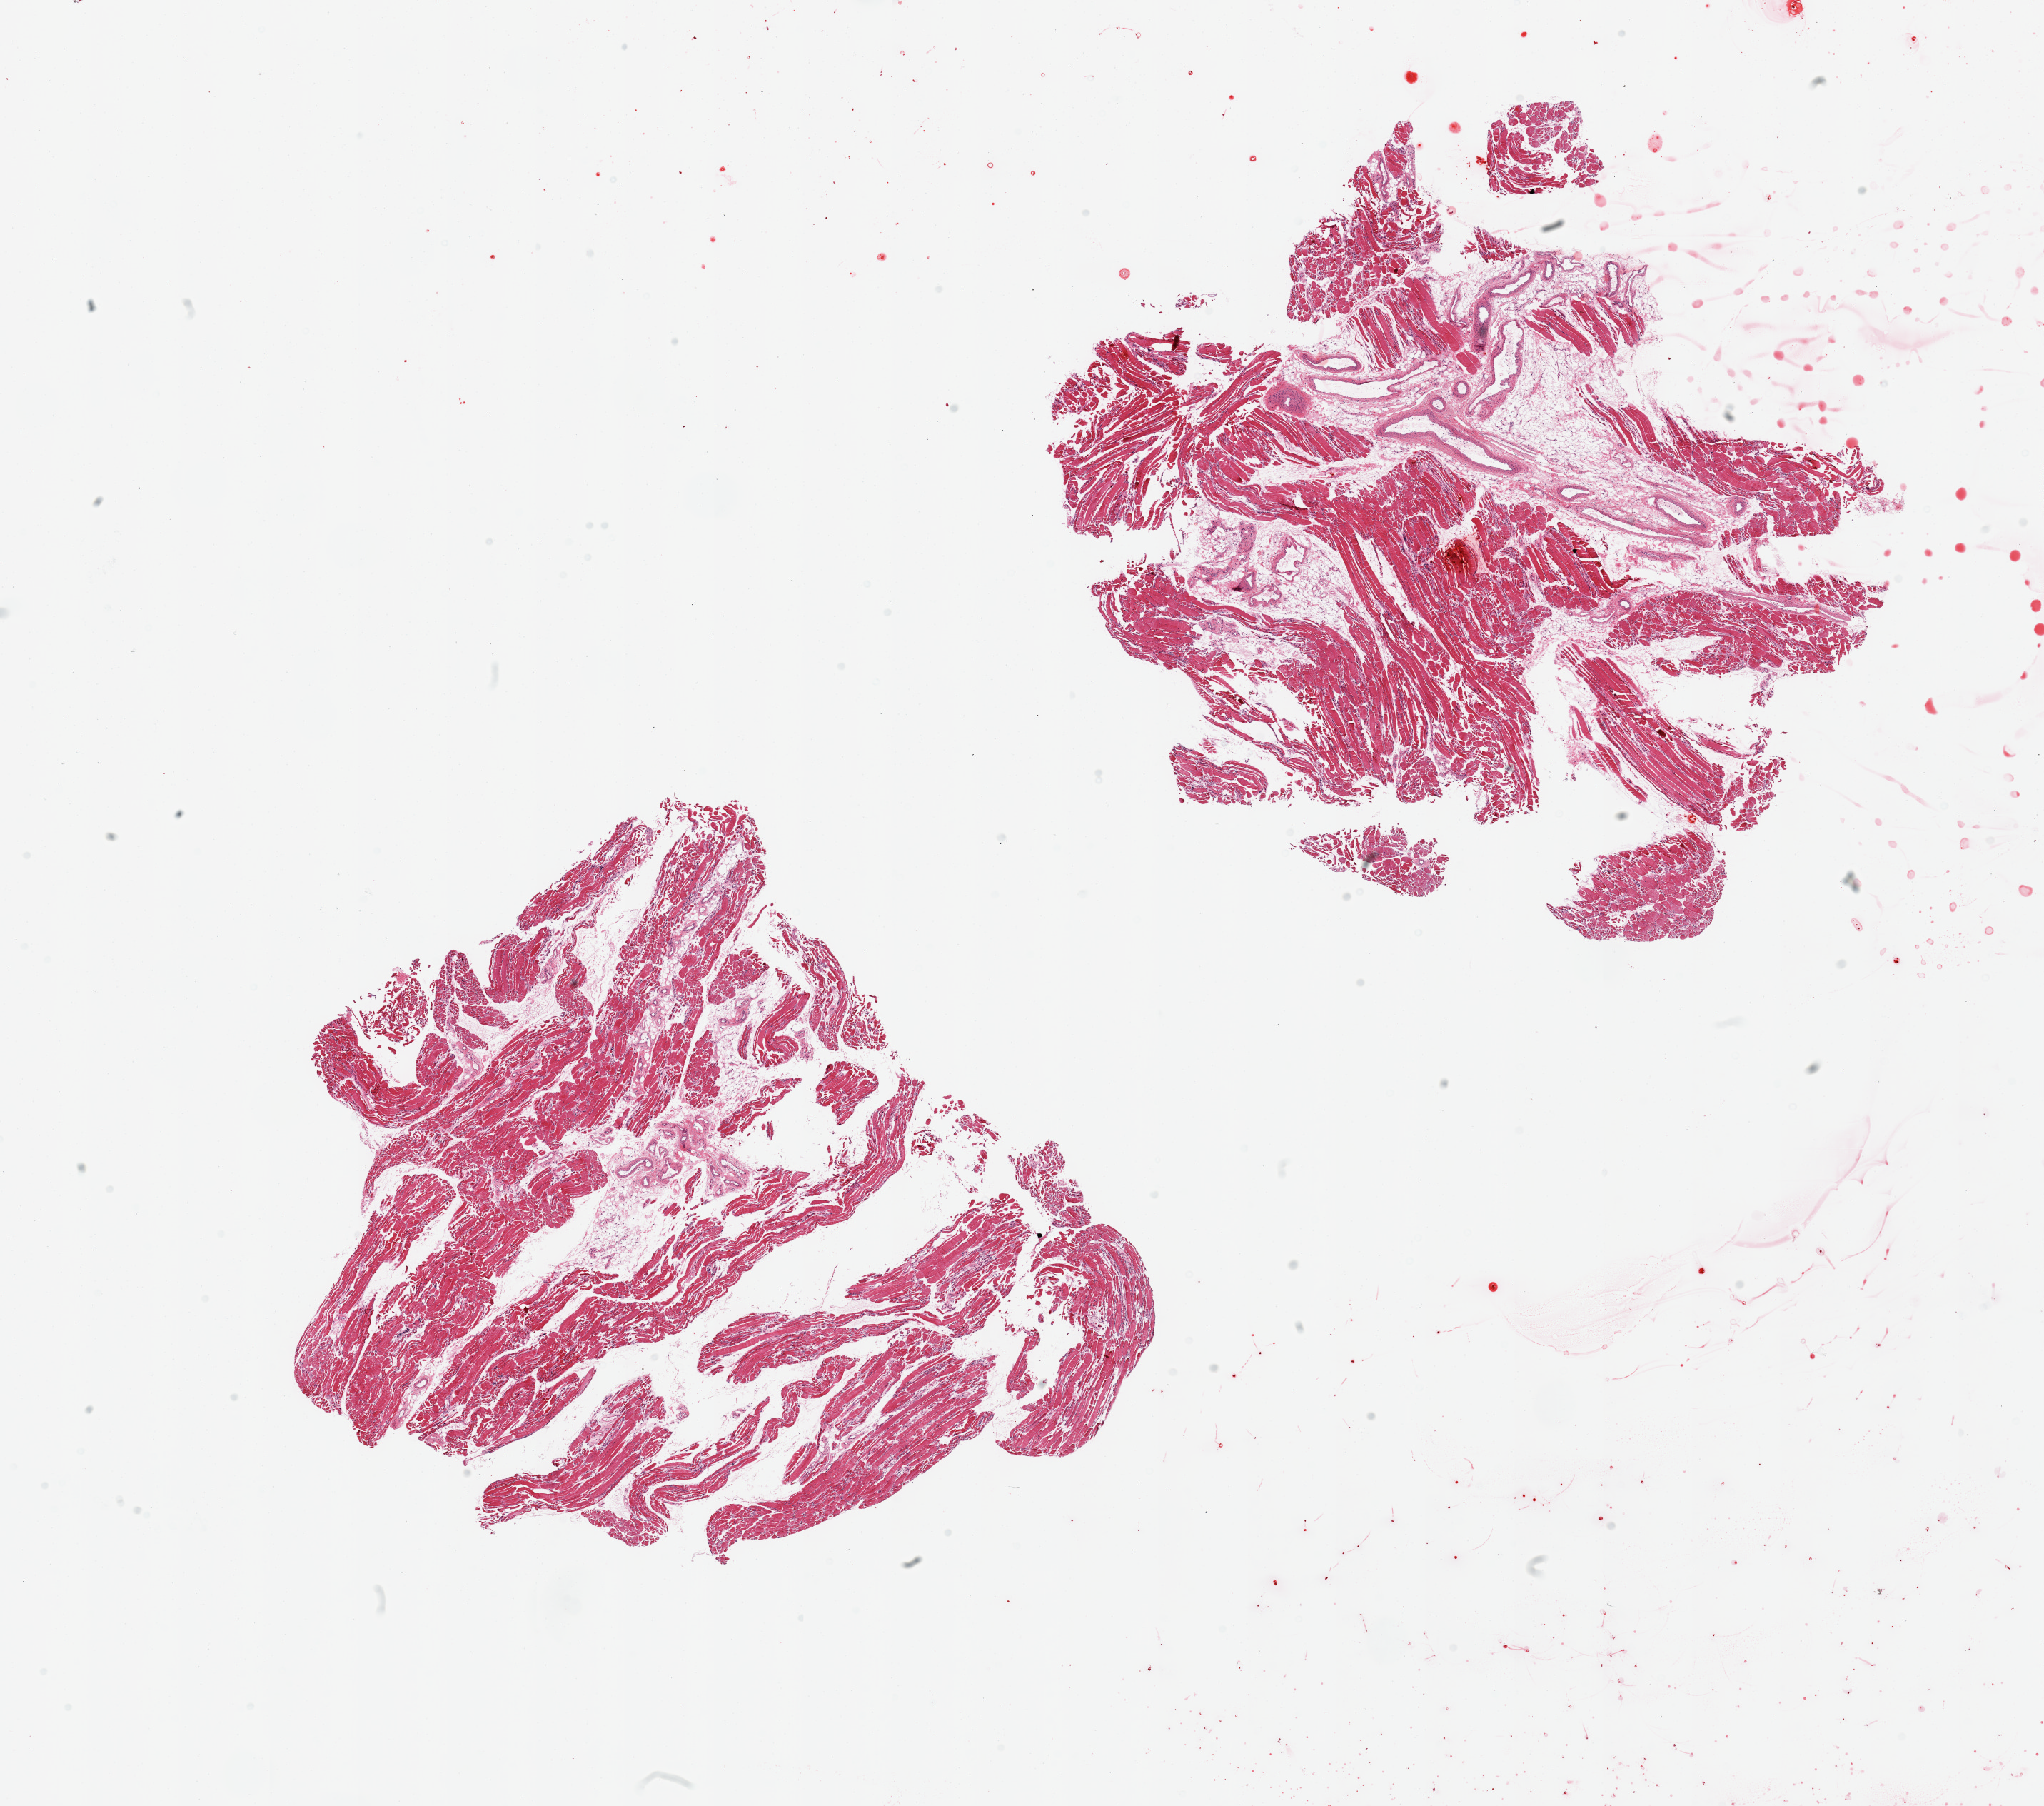
Haematoxylin and eosin whole-slide image, shown as a low-resolution overview of the whole scanned area (about 22.6 x 20.0 mm). PAXgene-fixed, paraffin-embedded tissue. Section of skeletal muscle (target tissue). Tissue donor sample. Donor: male.
Reviewer comment on this tissue sample: 2 pieces, atrophic, interstitial fat/vascular tisssue is ~30-40%.